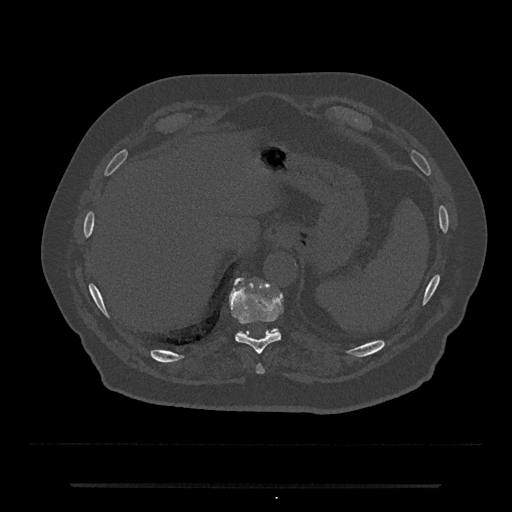
CT including the spine, one axial slice. Slice 696 of 797 in the series (ordered by position). Reconstruction kernel Br40s/3. Bone window (W 1800 / L 400 HU). 0.5 mm slice thickness. 512 × 512 image matrix, field of view 434 × 434 mm. Patient: male, 80 years. Case-level facts recorded for this patient, not image findings: primary cancer: prostate.
Outlined on this slice (semi-automatic segmentation, software-assisted and operator-edited):
- T10 vertebra: bounding box (x1, y1, x2, y2) in pixels: (229, 278, 282, 354)
- T11 vertebra: (270, 328, 279, 333)
- T9 vertebra: (256, 364, 264, 374)